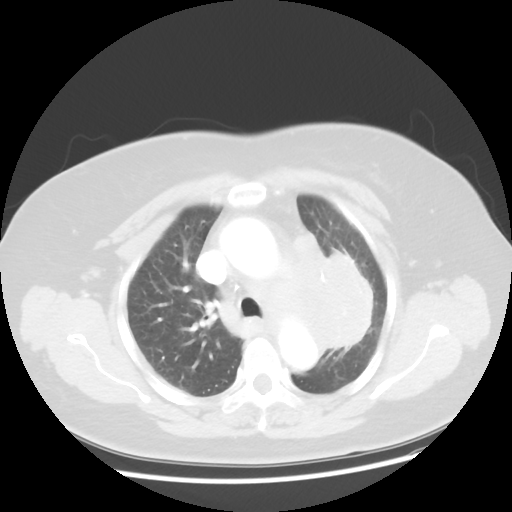
Chest CT, one axial slice. Position 33 of 49 along the scan axis. Lung window (W 1500 / L -600 HU). 5 mm slice thickness. 512 × 512 image matrix, field of view 374 × 374 mm. Female patient, age 58 years. Case-level facts recorded for this patient, not image findings: clinical TNM (as recorded): T4 N3 M0; histopathological grade: G3.
Outlined on this slice (rectangle marked by the reading radiologist):
- lung tumour (recorded histology: small cell carcinoma): box from (x=281, y=216) to (x=381, y=367) px